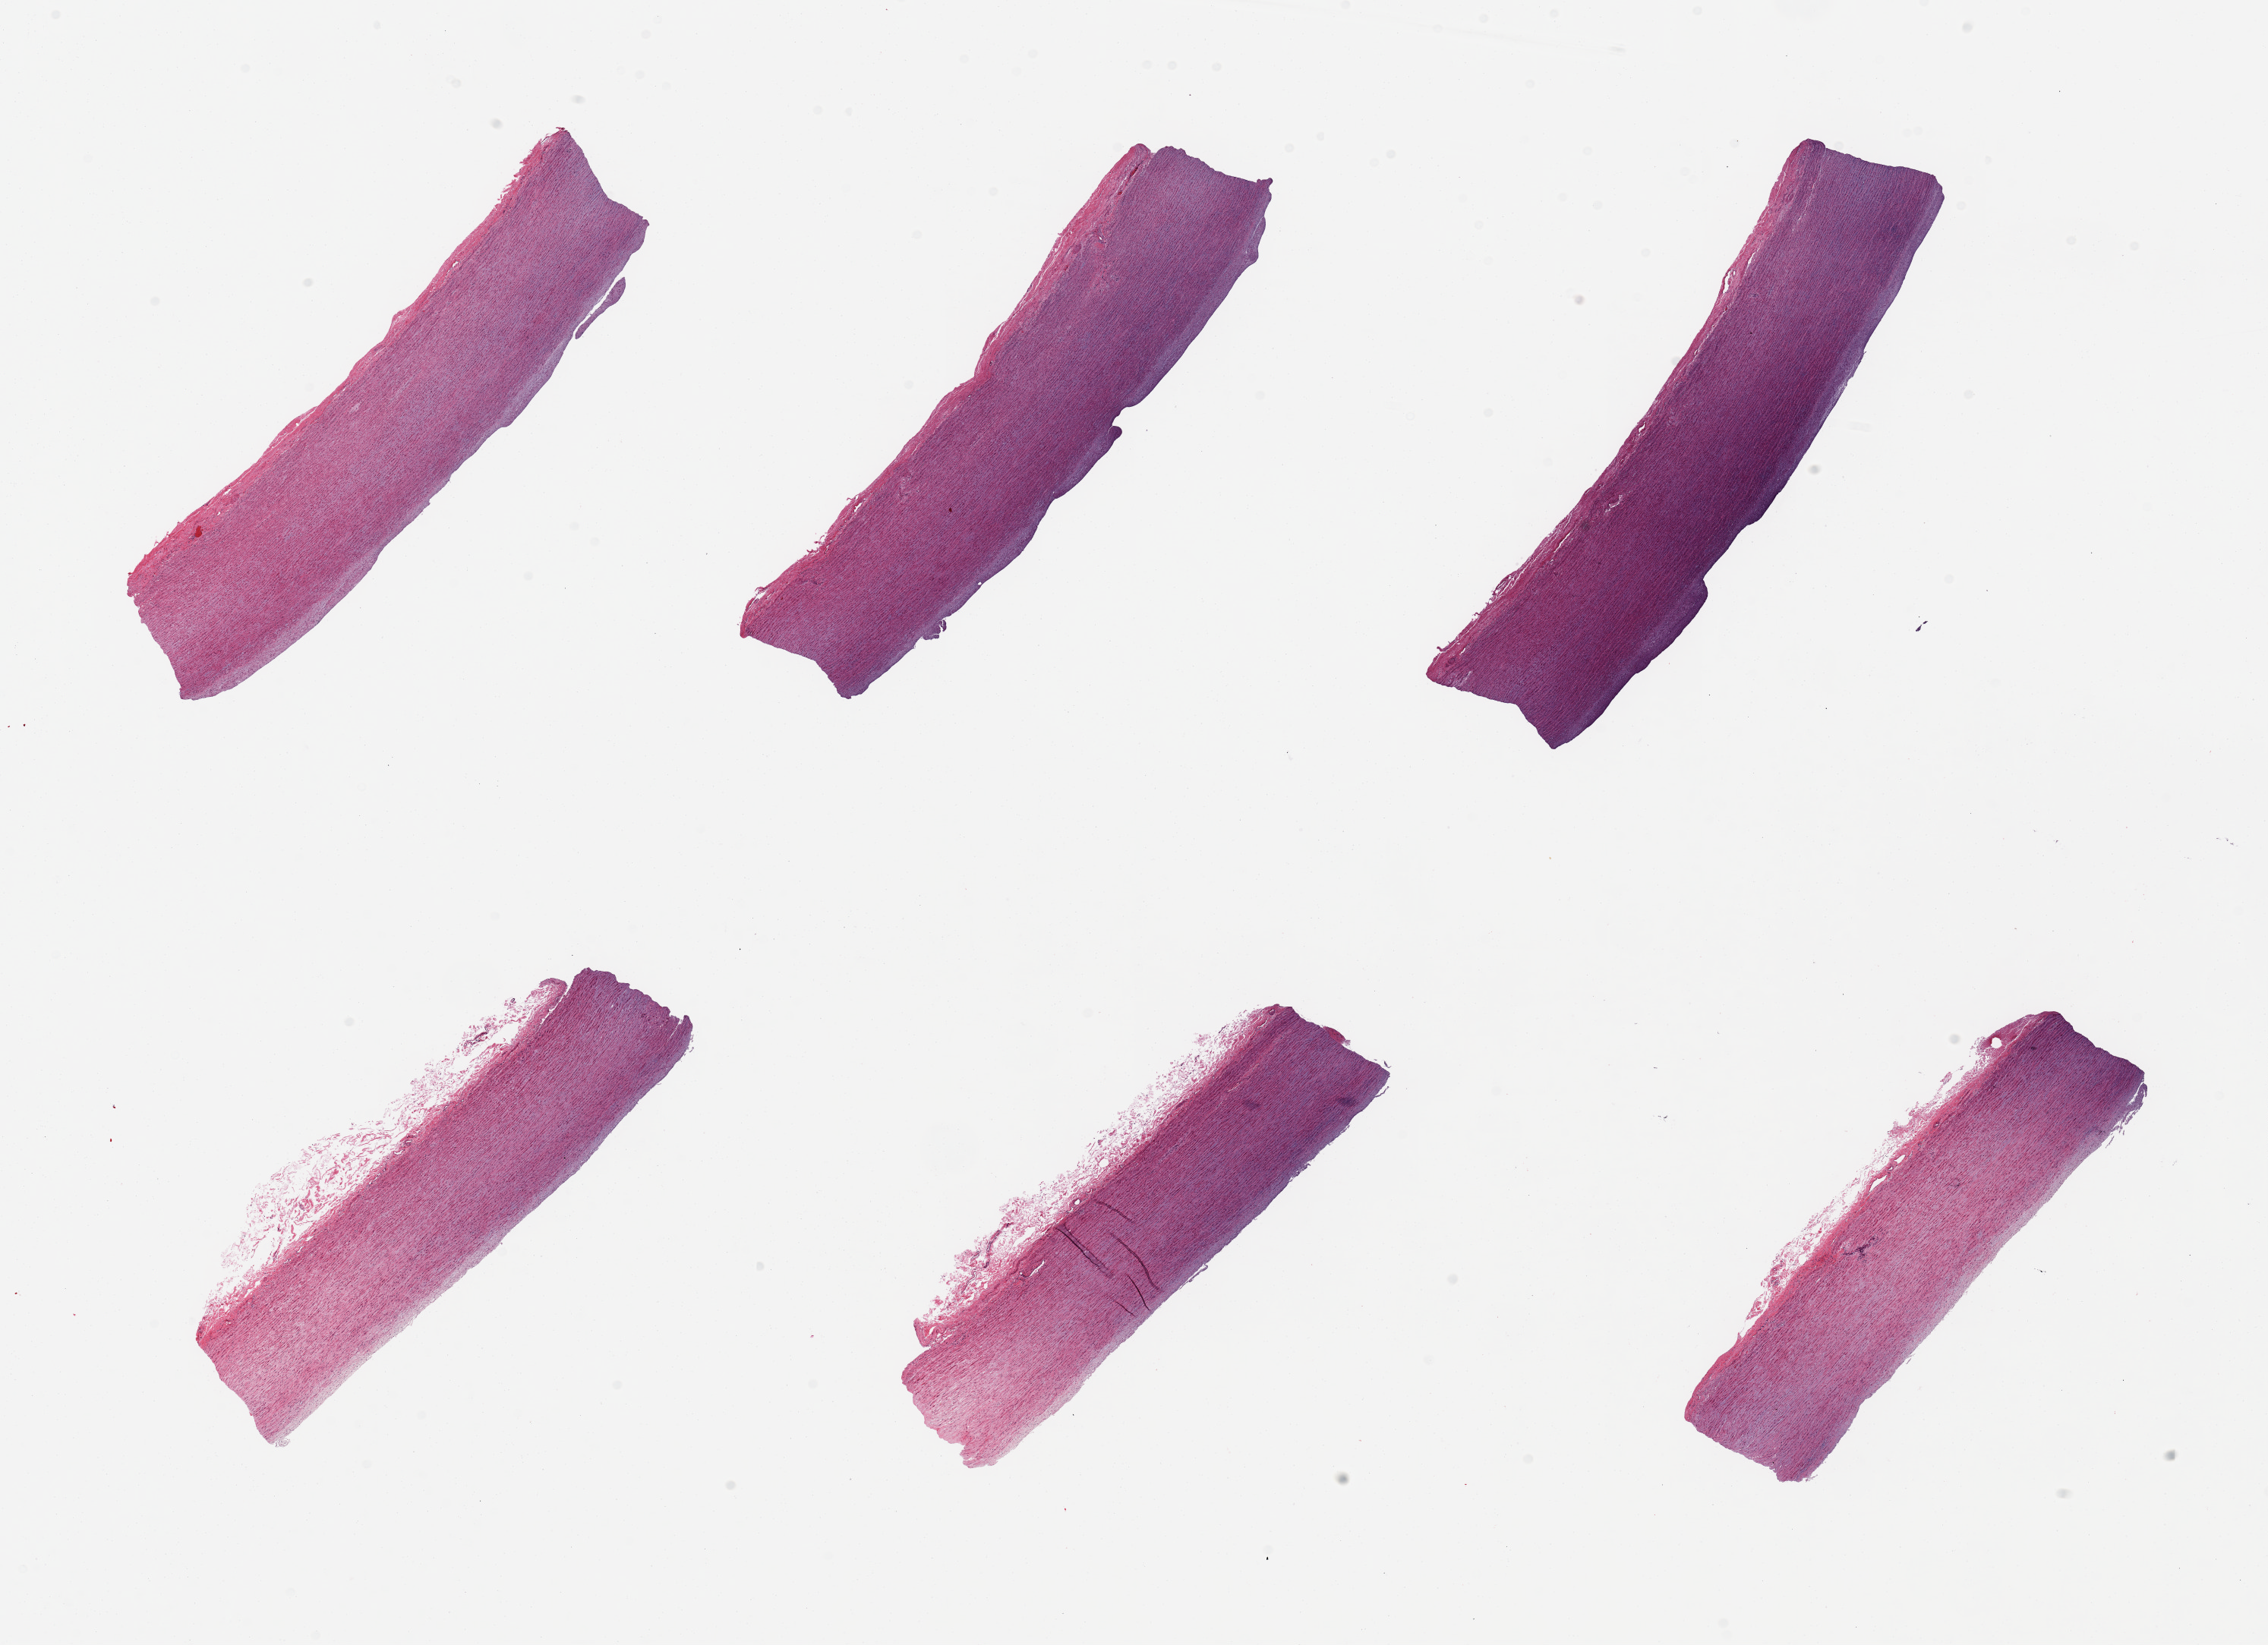
Digitized H&E-stained section — whole scanned area (about 23.6 x 17.1 mm) shown as a low-resolution overview, PAXgene-fixed, paraffin-embedded tissue, section of aorta (target tissue), donor tissue sample. Donor sex: female.
Review note (as recorded): 6 pieces; early sclerotic plaque formation.